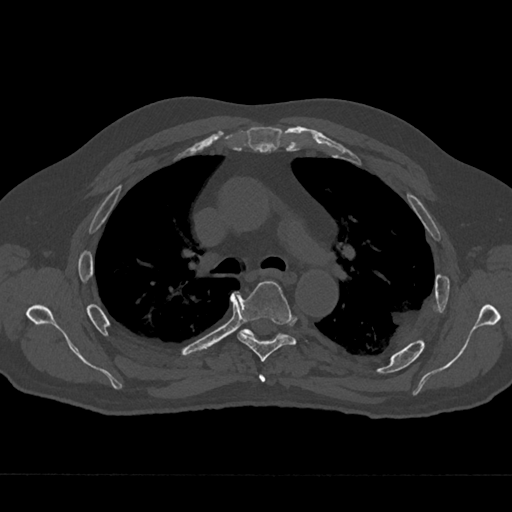
CT including the spine, one axial slice. Slice 466 of 797 in the series (ordered by position). Reconstruction kernel Br40s/3. 120 kVp. Bone window (W 1800 / L 400 HU). 512 × 512 image matrix. Male patient, age 75 years. Case-level facts recorded for this patient, not image findings: primary cancer: renal; vertebrae with lytic lesions (as recorded): T4.
Annotated regions visible in this slice (semi-automatic segmentation, software-assisted and operator-edited):
- T4 vertebra: bounding box [x1, y1, x2, y2] px = [259, 374, 266, 382]
- T5 vertebra: [237, 281, 308, 362]
- T6 vertebra: [240, 328, 254, 337]